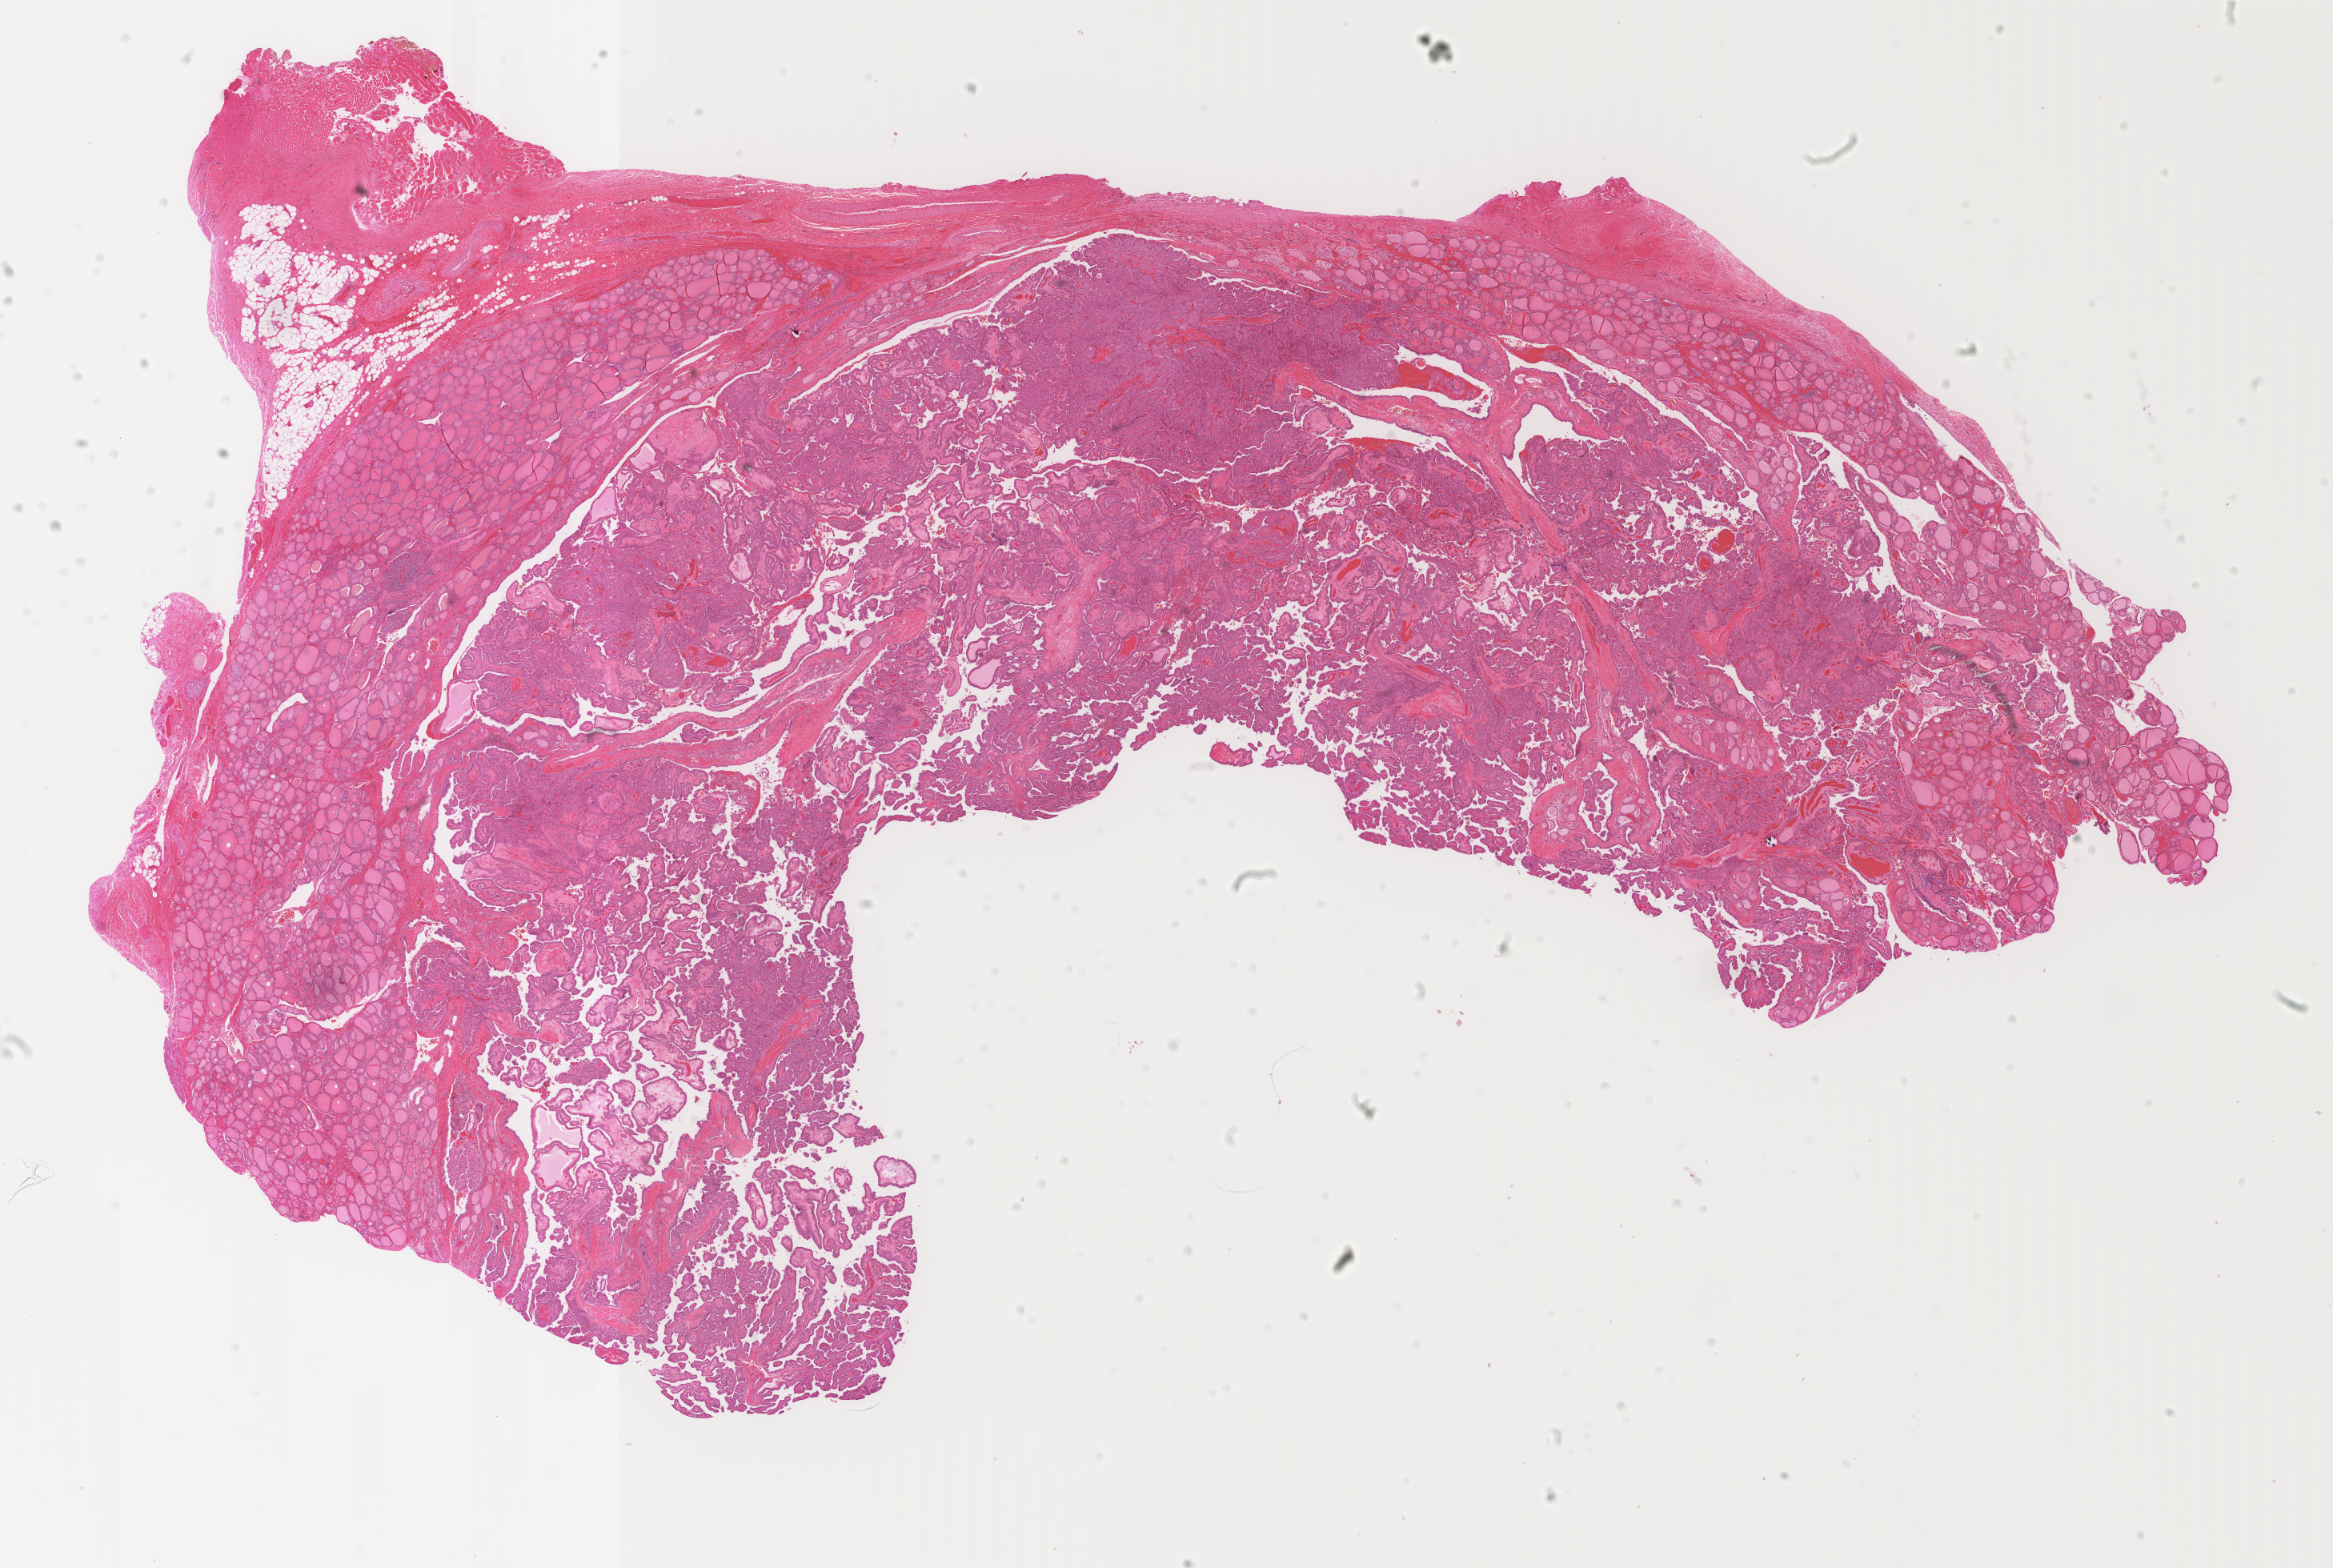
H&E whole-slide image, whole scanned area (about 23.1 x 15.5 mm, acquisition: 40x scan) shown as a low-resolution overview. Formalin-fixed paraffin-embedded (FFPE) diagnostic section. Thyroid, primary tumour sample. Patient: female, age at initial diagnosis 37 years.
- histologic diagnosis: Papillary adenocarcinoma, NOS (thyroid gland)
- lymph nodes positive (case pathology): 1 of 1 examined
- AJCC pathologic stage: I
- laterality: bilateral